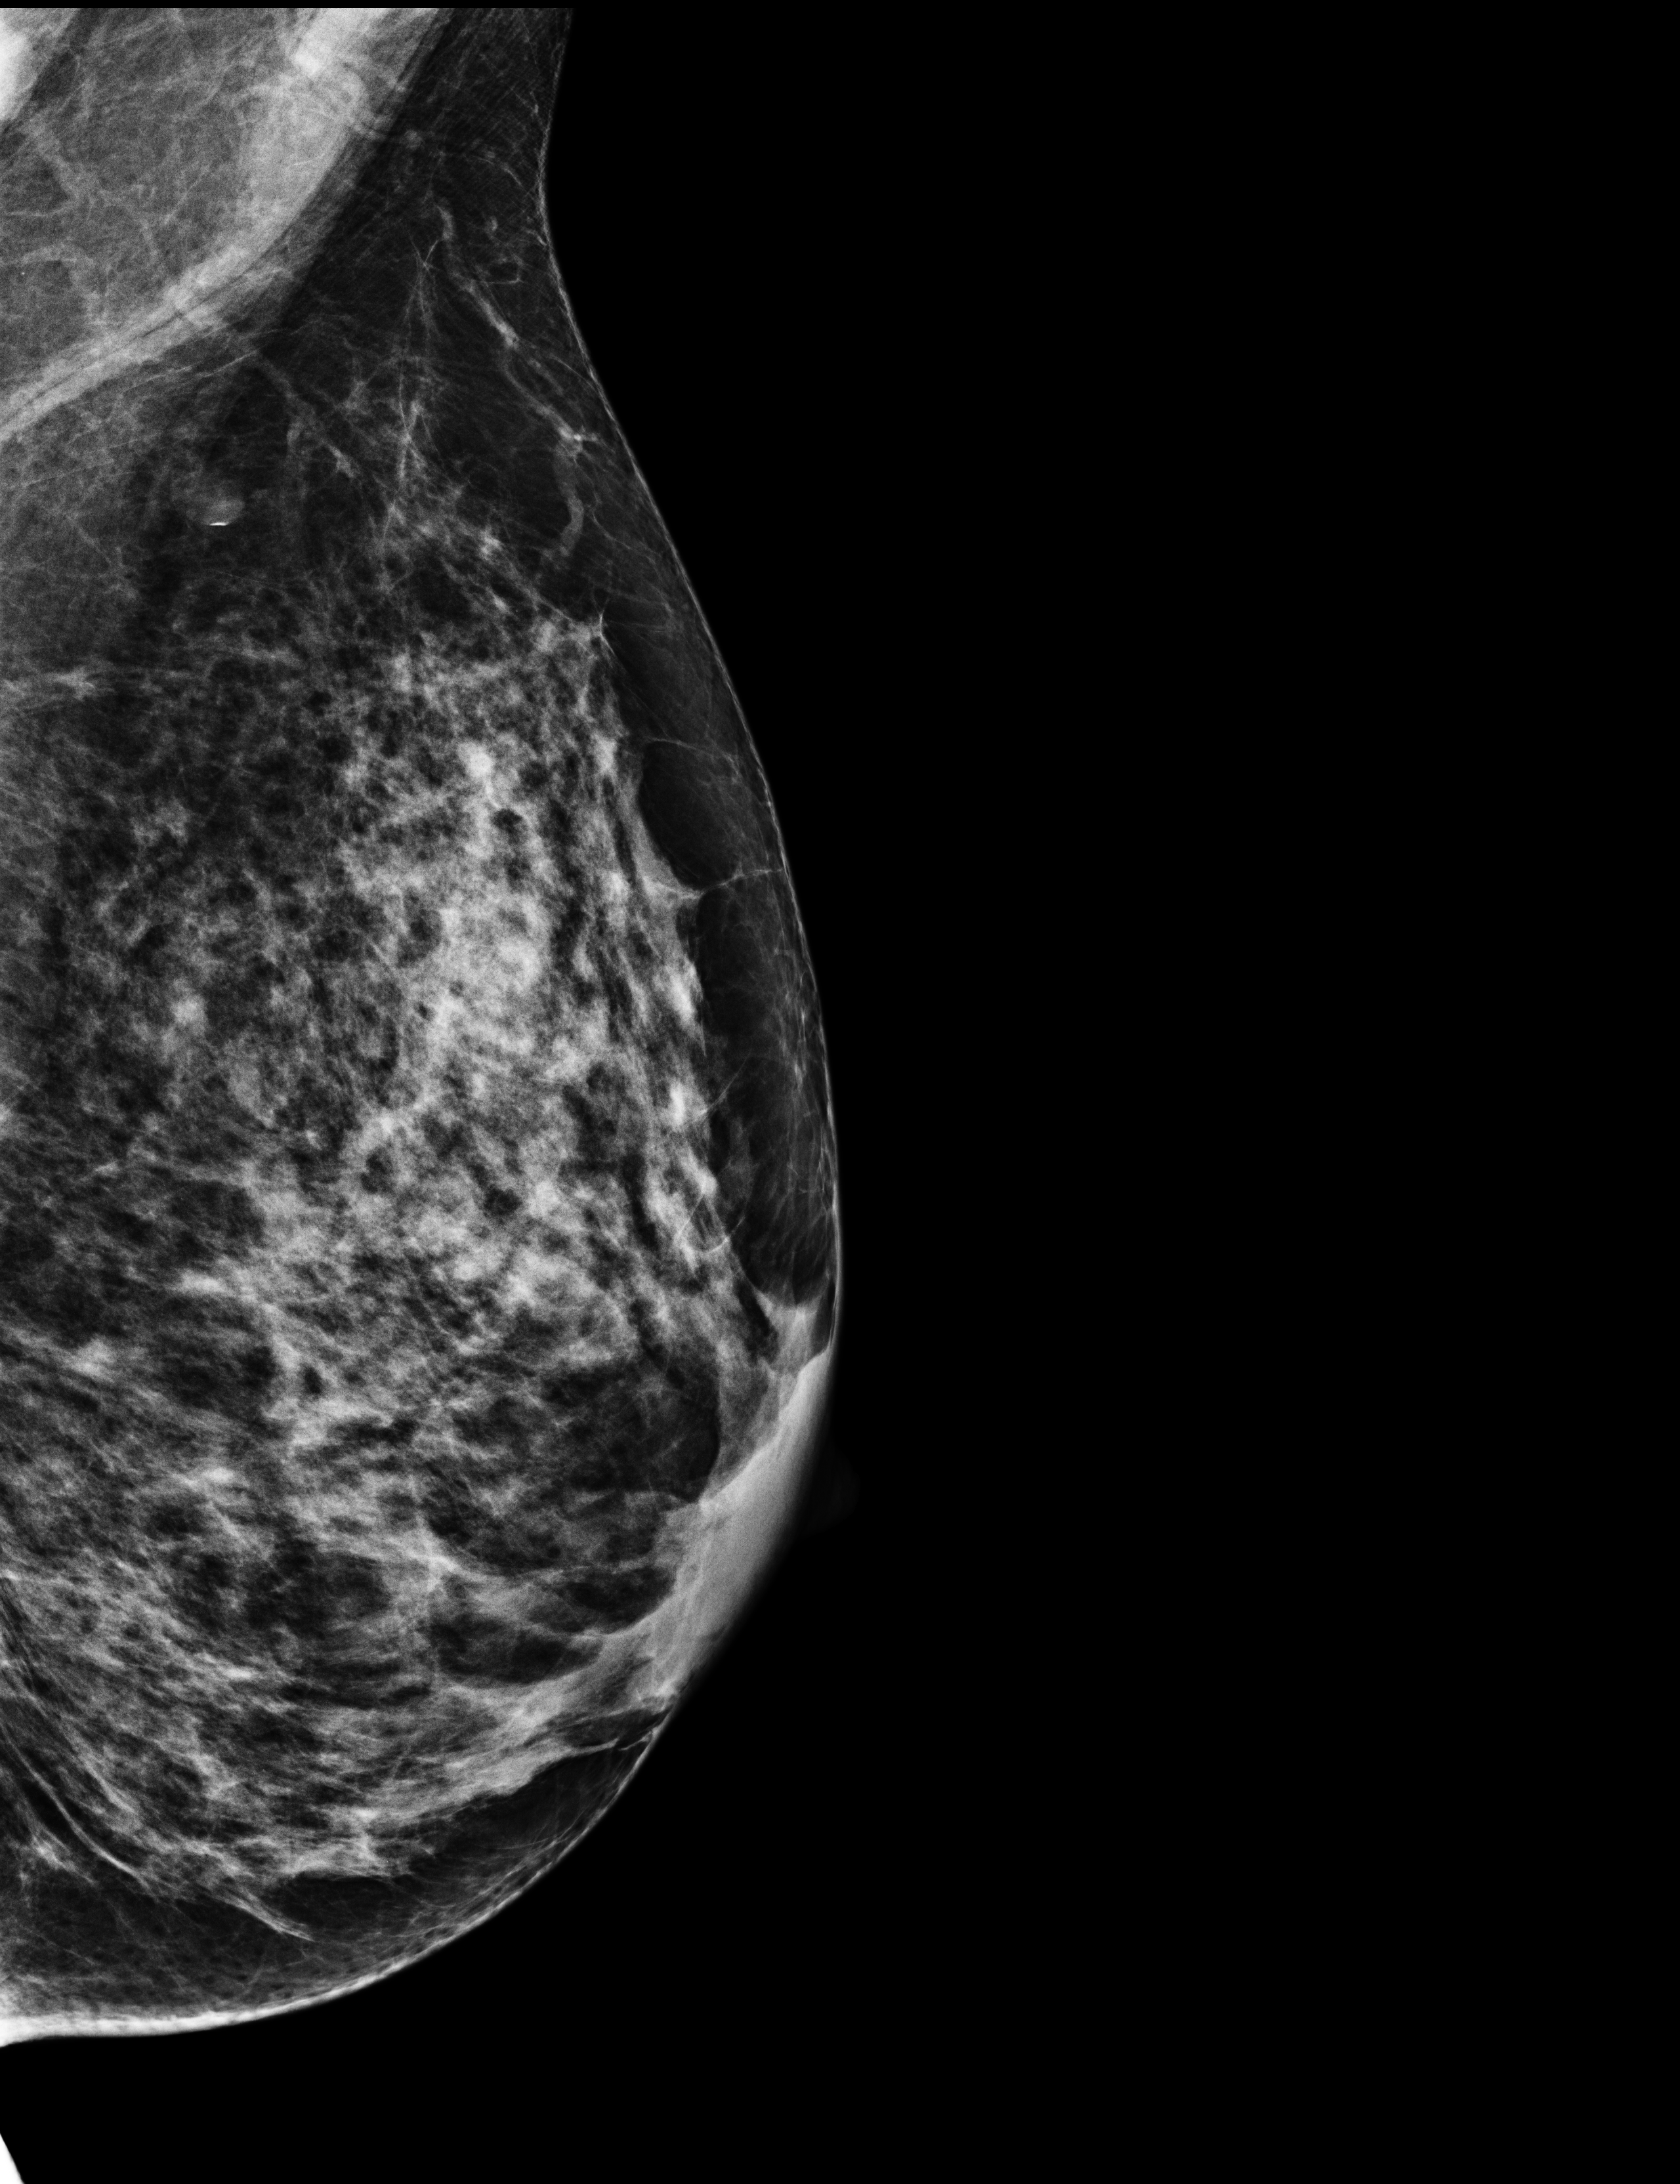
Full-field digital mammogram (FFDM), left breast, mediolateral oblique (MLO) view, screening examination. Female patient, age 59 years.
Breast density at the screening exam (both breasts): heterogeneously dense (BI-RADS density category c). Final BI-RADS assessment for this screening round (tomosynthesis exam, both breasts): category 1. Recall: no recall after this screen.